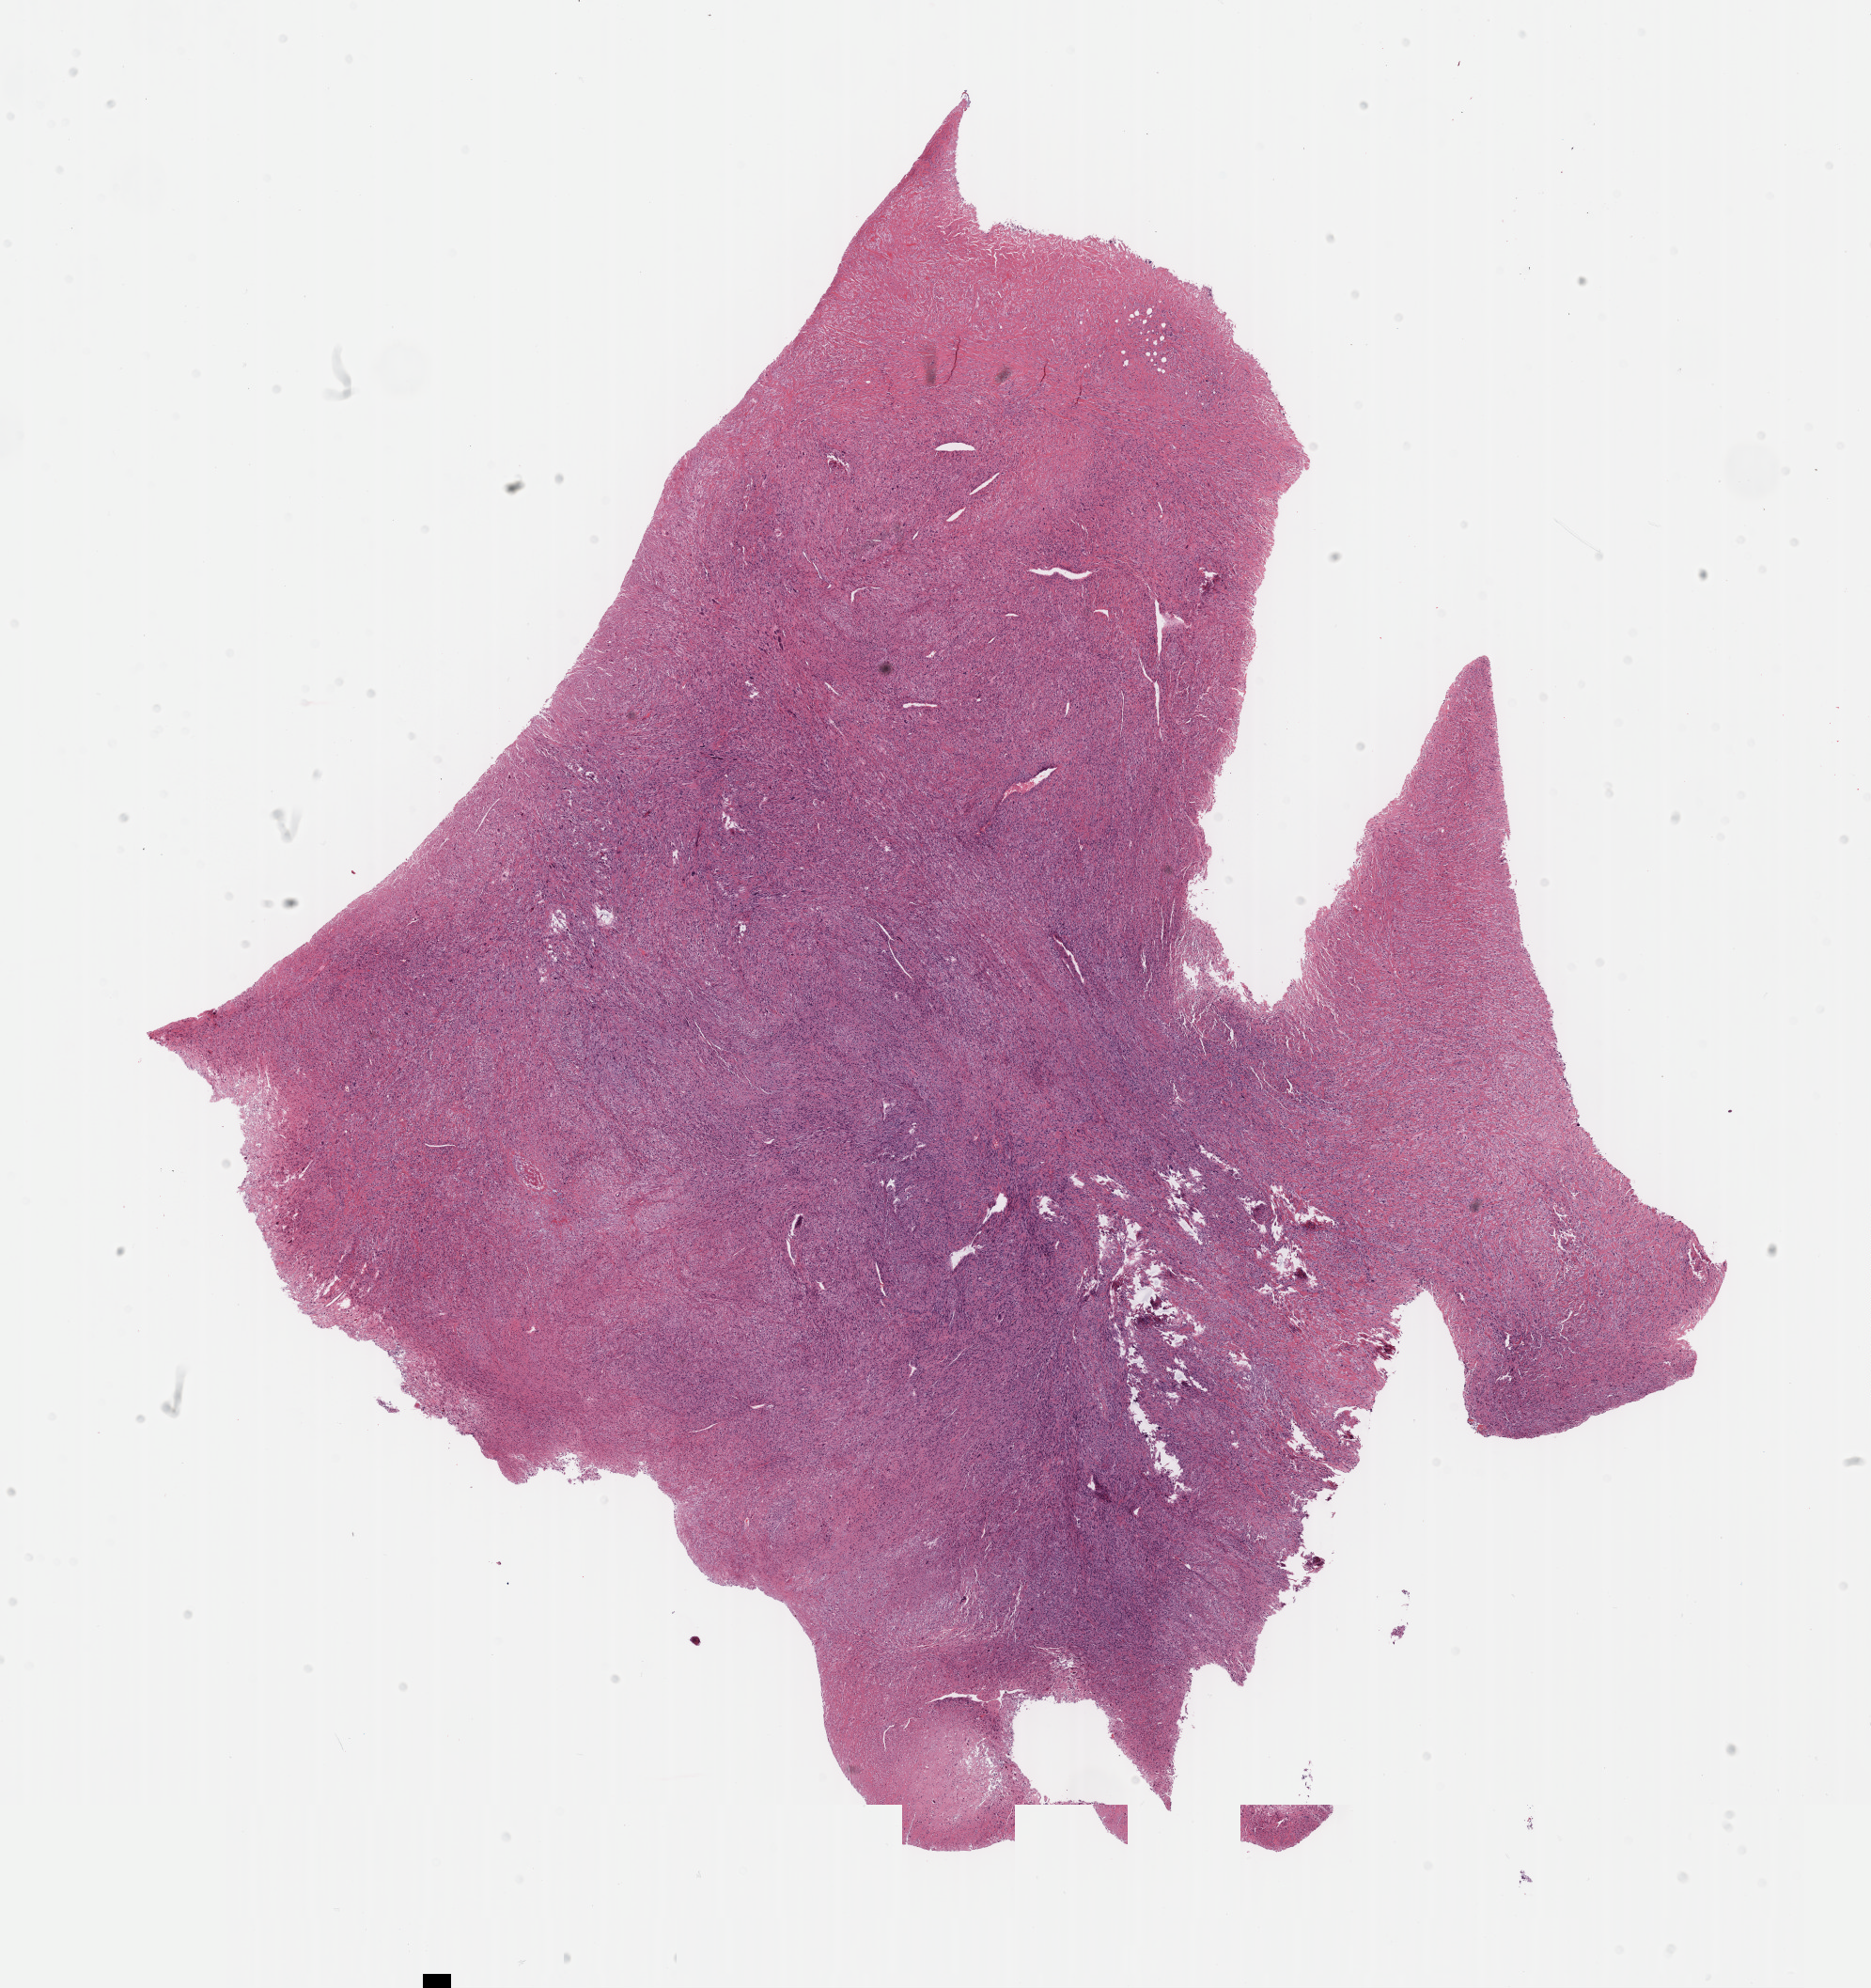
H&E whole-slide image, whole scanned area (about 16.1 x 17.1 mm, from a 40x scan) shown as a low-resolution overview. FFPE section. Sample: primary tumour, connective, subcutaneous and other soft tissues. Male patient; age at initial diagnosis 58 years.
- histologic diagnosis: Malignant fibrous histiocytoma (connective, subcutaneous and other soft tissues of lower limb and hip)